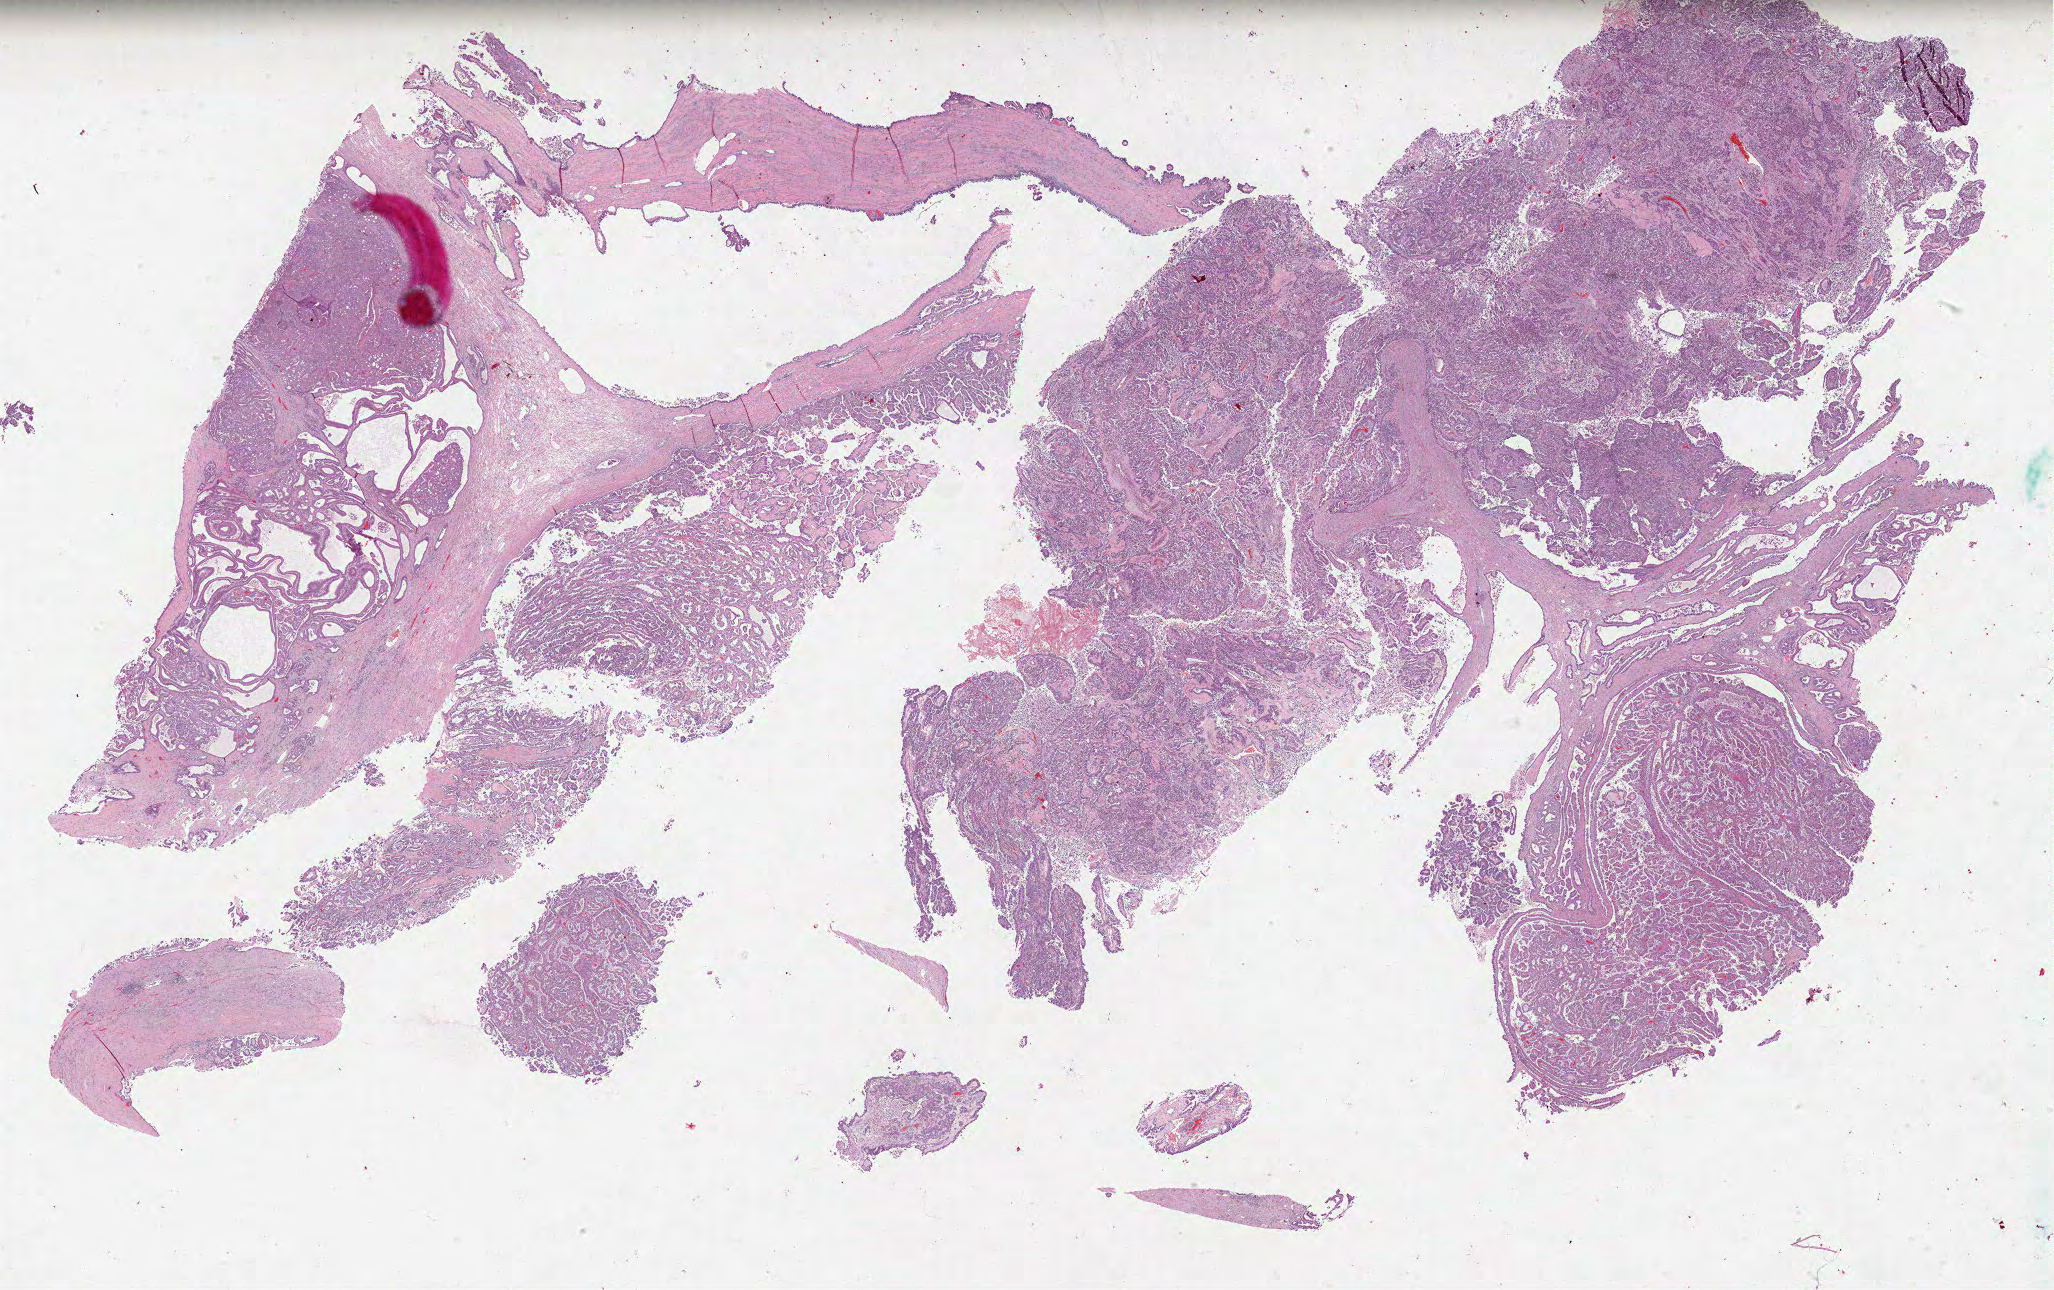
Digitized H&E tissue section (whole slide) — a low-resolution overview of the entire scanned area, about 32.8 x 20.6 mm (from a 40x scan); formalin-fixed paraffin-embedded (FFPE) diagnostic section; kidney, primary tumour sample. Patient: male, age at initial diagnosis 61 years.
Diagnosis: Papillary adenocarcinoma, NOS.